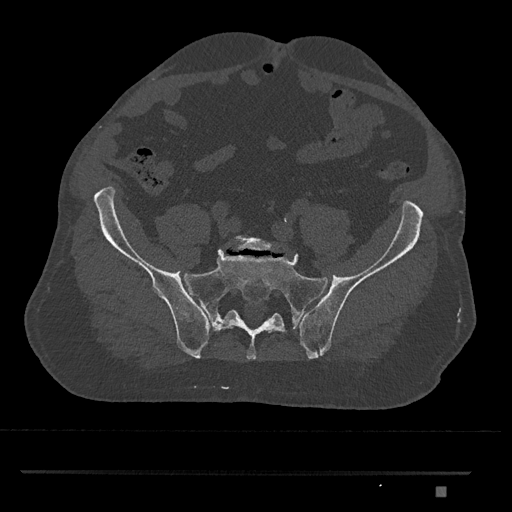
CT including the spine, one axial slice; slice 496 of 1134 in the series (ordered by position); reconstruction kernel Br40s/3; 120 kVp; bone window (W 1800 / L 400 HU); 0.5 mm slice thickness; 512 × 512 image matrix, field of view 429 × 429 mm. Patient: male, 65 years. From the clinical record (not read from this slice): primary cancer: prostate.
Structures marked on this image (semi-automatic segmentation, software-assisted and operator-edited):
- L5 vertebra: bounding box (x1, y1, x2, y2) in pixels: (233, 236, 280, 251)